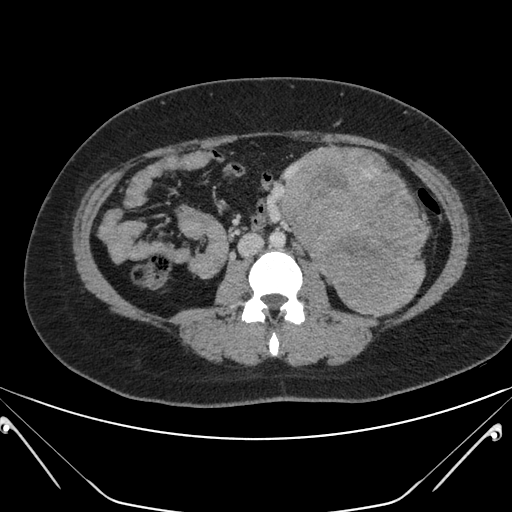
Contrast-enhanced abdominal CT, one axial slice; slice 93 of 168 in the series (ordered by position); 120 kVp; intravenous contrast given; soft-tissue window (W 400 / L 40 HU); 3 mm slice thickness; 512 × 512 image matrix, field of view 394 × 394 mm. Patient: female, 26 years. Case-level facts recorded for this patient, not image findings: diagnosis: adrenocortical carcinoma; tumour side: left adrenal; tumour size at pathology: 28 cm; Ki-67 index: 20 %; stage (as recorded): 2.
Outlined on this slice (semi-automatic segmentation, software-assisted and operator-edited):
- mass: box from (x=284, y=150) to (x=425, y=313) px